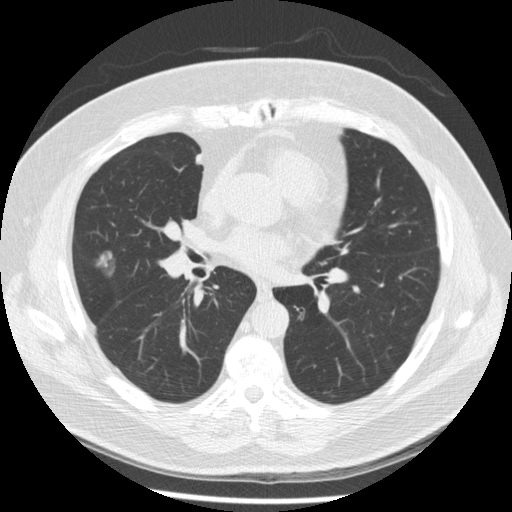
Axial slice from a low-dose chest CT screening exam. Second annual screen. Lung window (W 1500 / L -600 HU). Standard (soft-tissue) reconstruction kernel (STANDARD). Slice 115 of 230 in the series. Male participant, aged 67 years at enrolment.
Lesion marked by an expert reader, bounding box (x1, y1, x2, y2) in pixels: (83, 245, 123, 287). Screening reader's record for this exam (one nodule recorded; not confirmed to be the boxed lesion): non-calcified nodule or mass ≥4 mm, right middle lobe, 19 × 16 mm, smooth margins, soft tissue attenuation, pre-existing on the prior screen: yes; interval growth: yes. Lung cancer was diagnosed 47 days after this screen: adenocarcinoma, NOS, right middle lobe, moderately differentiated (G2), stage IA (AJCC 6th edition), 14 mm at pathology.